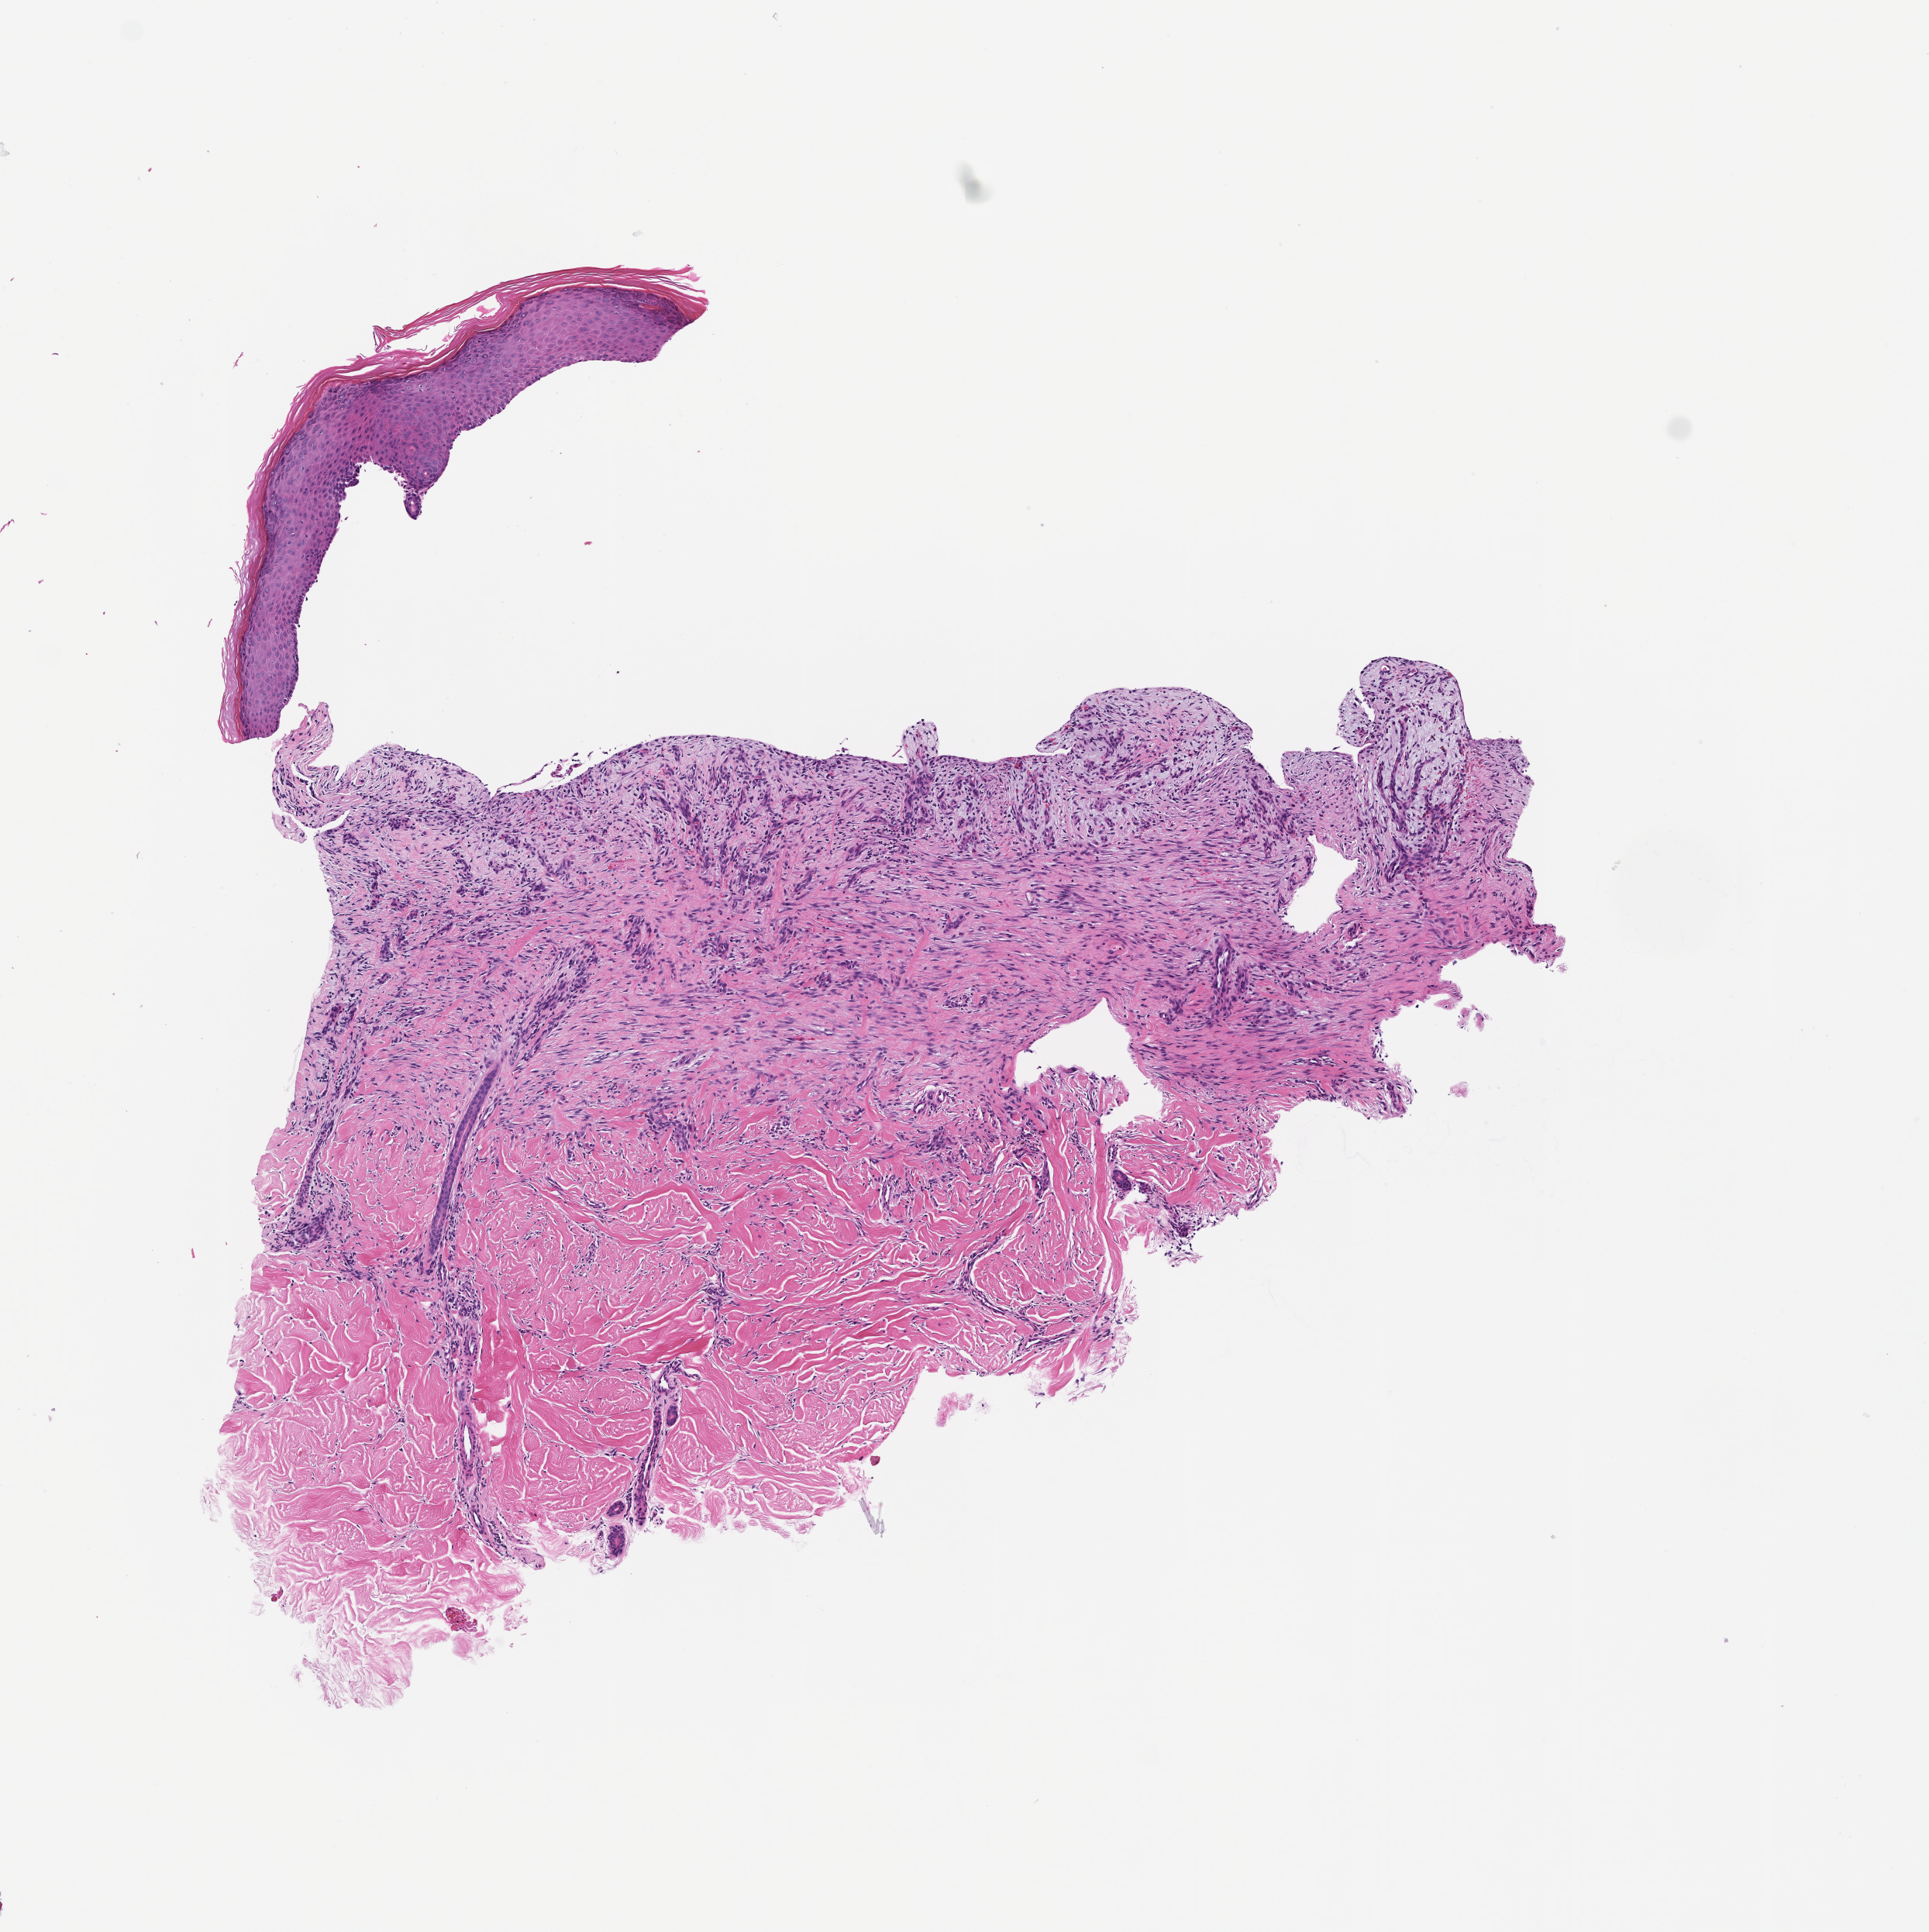
Haematoxylin and eosin whole-slide image — a low-resolution overview of the entire scanned area, about 5.0 x 5.0 mm, formalin-fixed, paraffin-embedded (FFPE) tissue, site: skin. Patient: male.
This section: primary tumour tissue. Diagnosis: Melanoma.